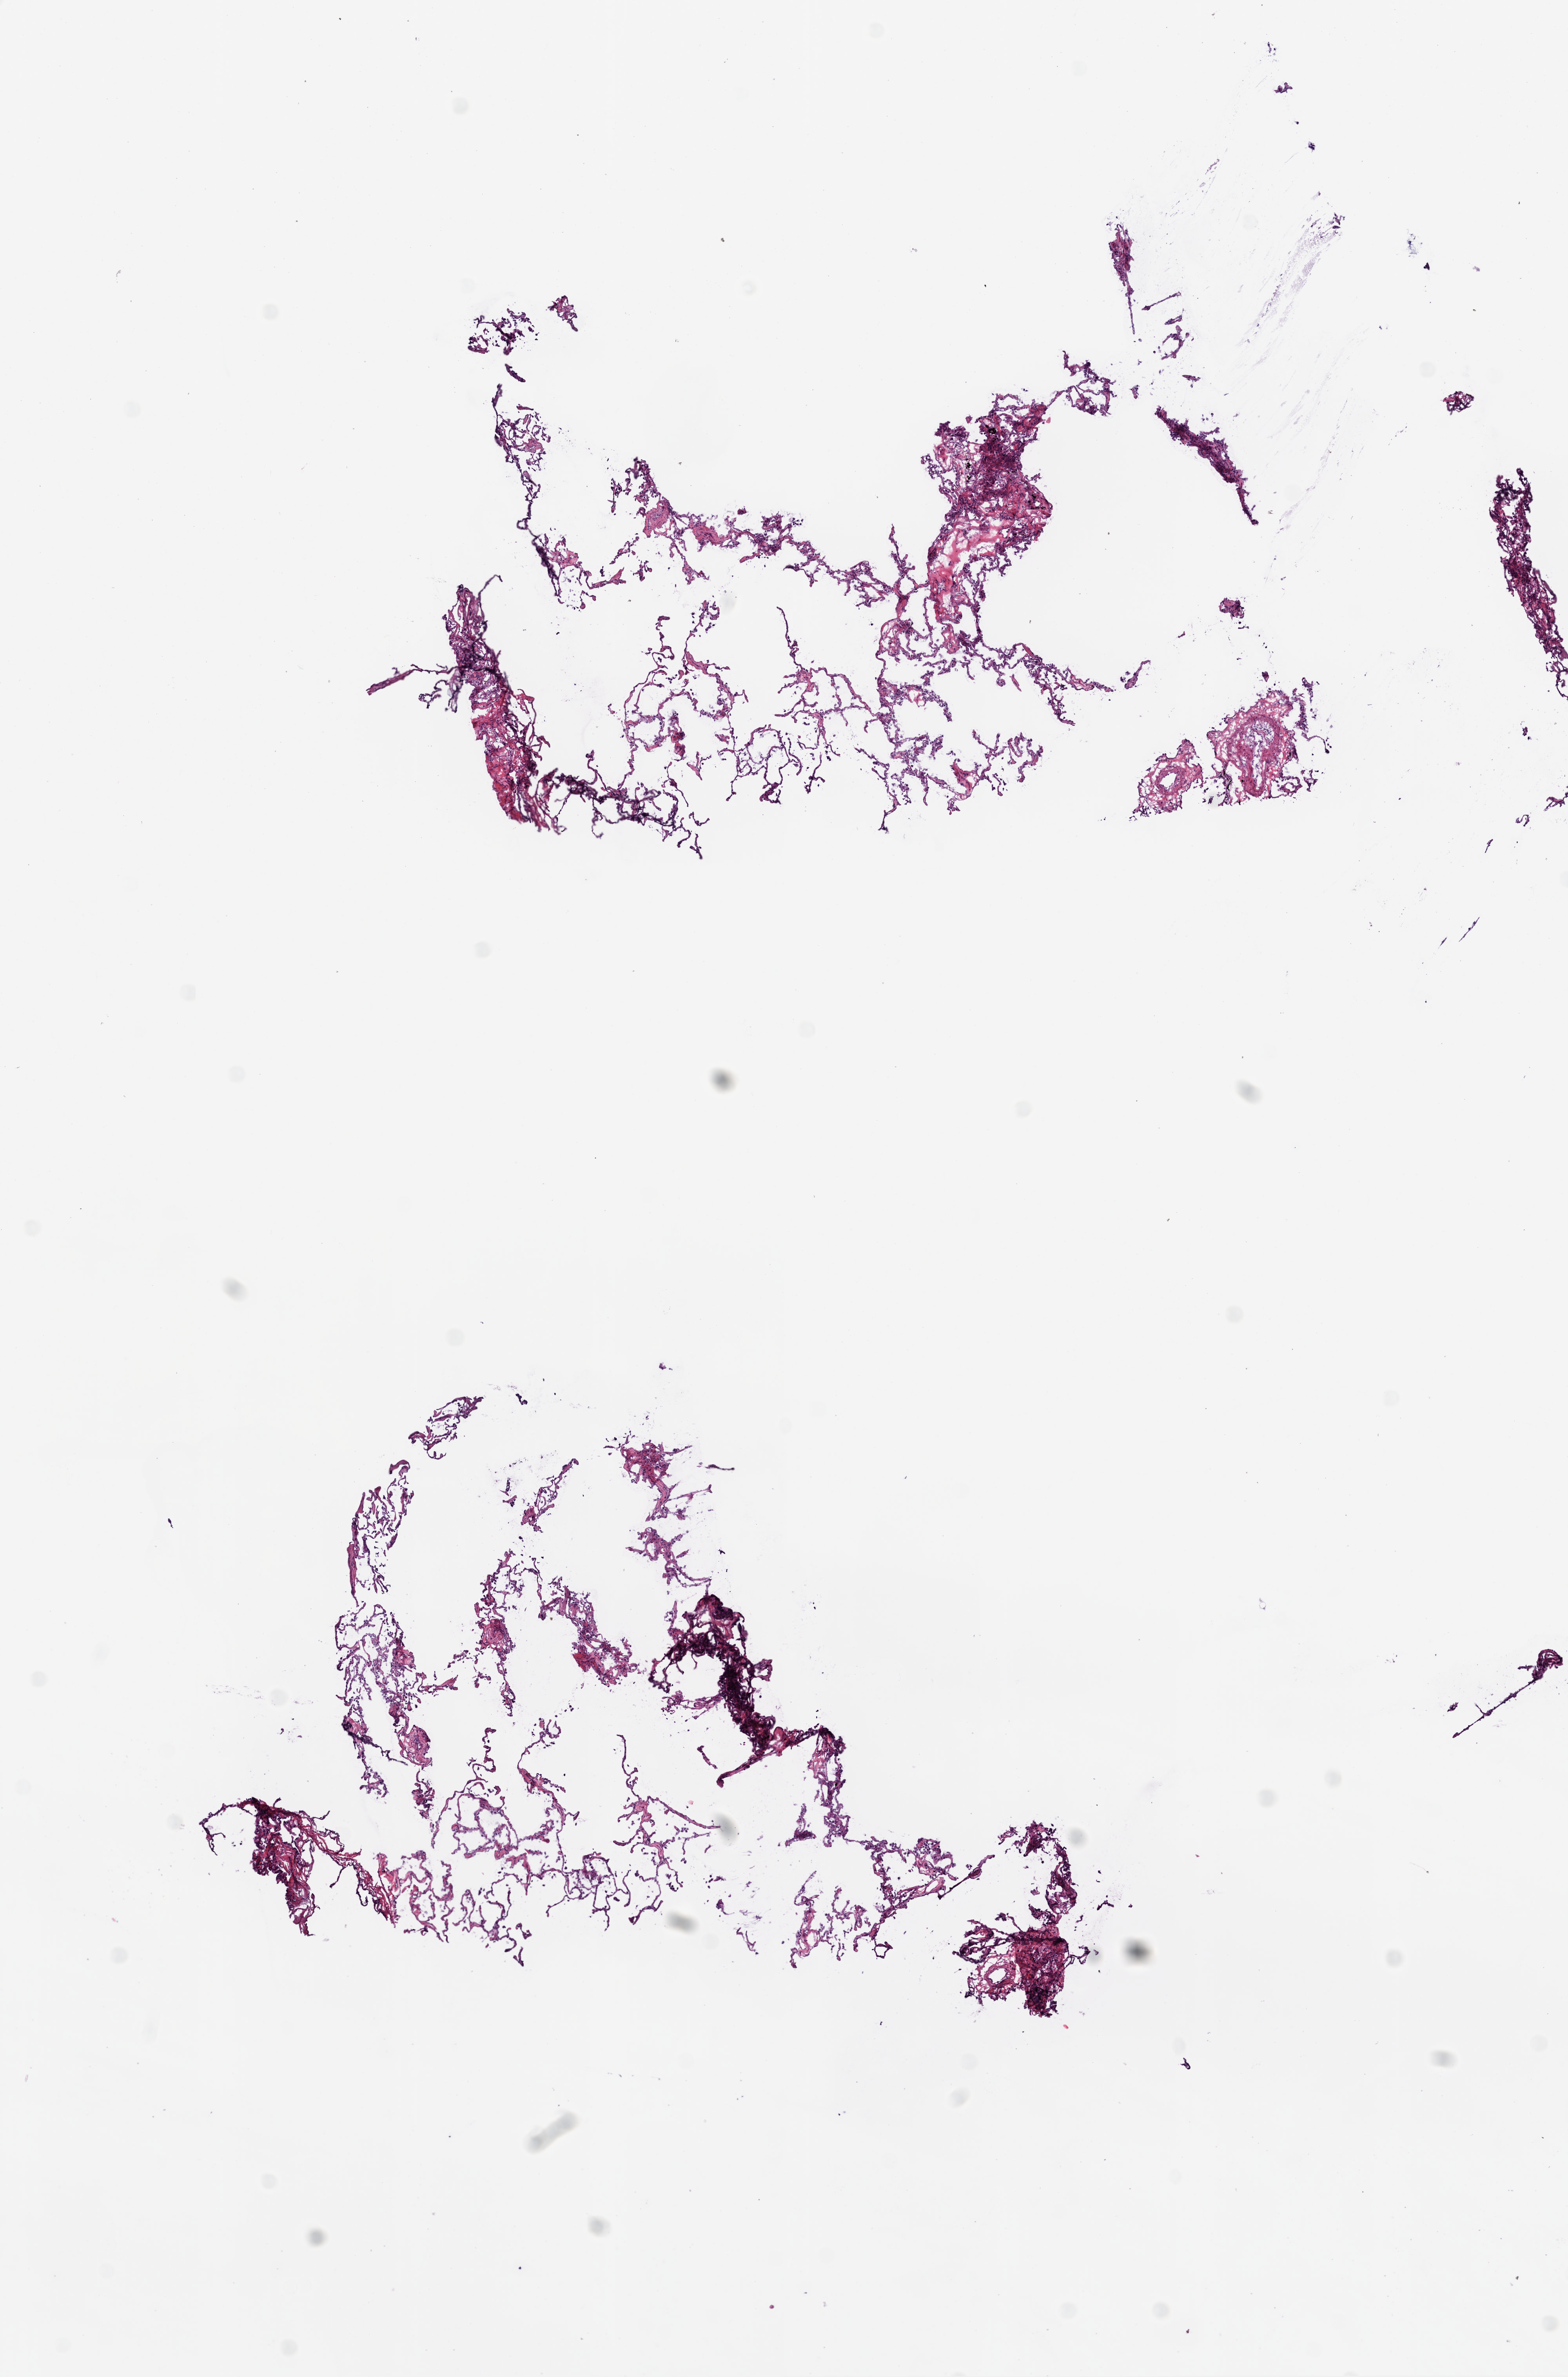
Digitized H&E-stained tissue section (whole slide) — shown as a low-resolution overview of the whole scanned area (about 8.0 x 12.2 mm), frozen section from the bottom of the tissue portion, lung, solid tissue normal (non-tumour tissue) sample. Male, age 65 years at initial diagnosis.
This section: solid tissue normal sample (biorepository sample class). Patient diagnosis: Squamous cell carcinoma, NOS.